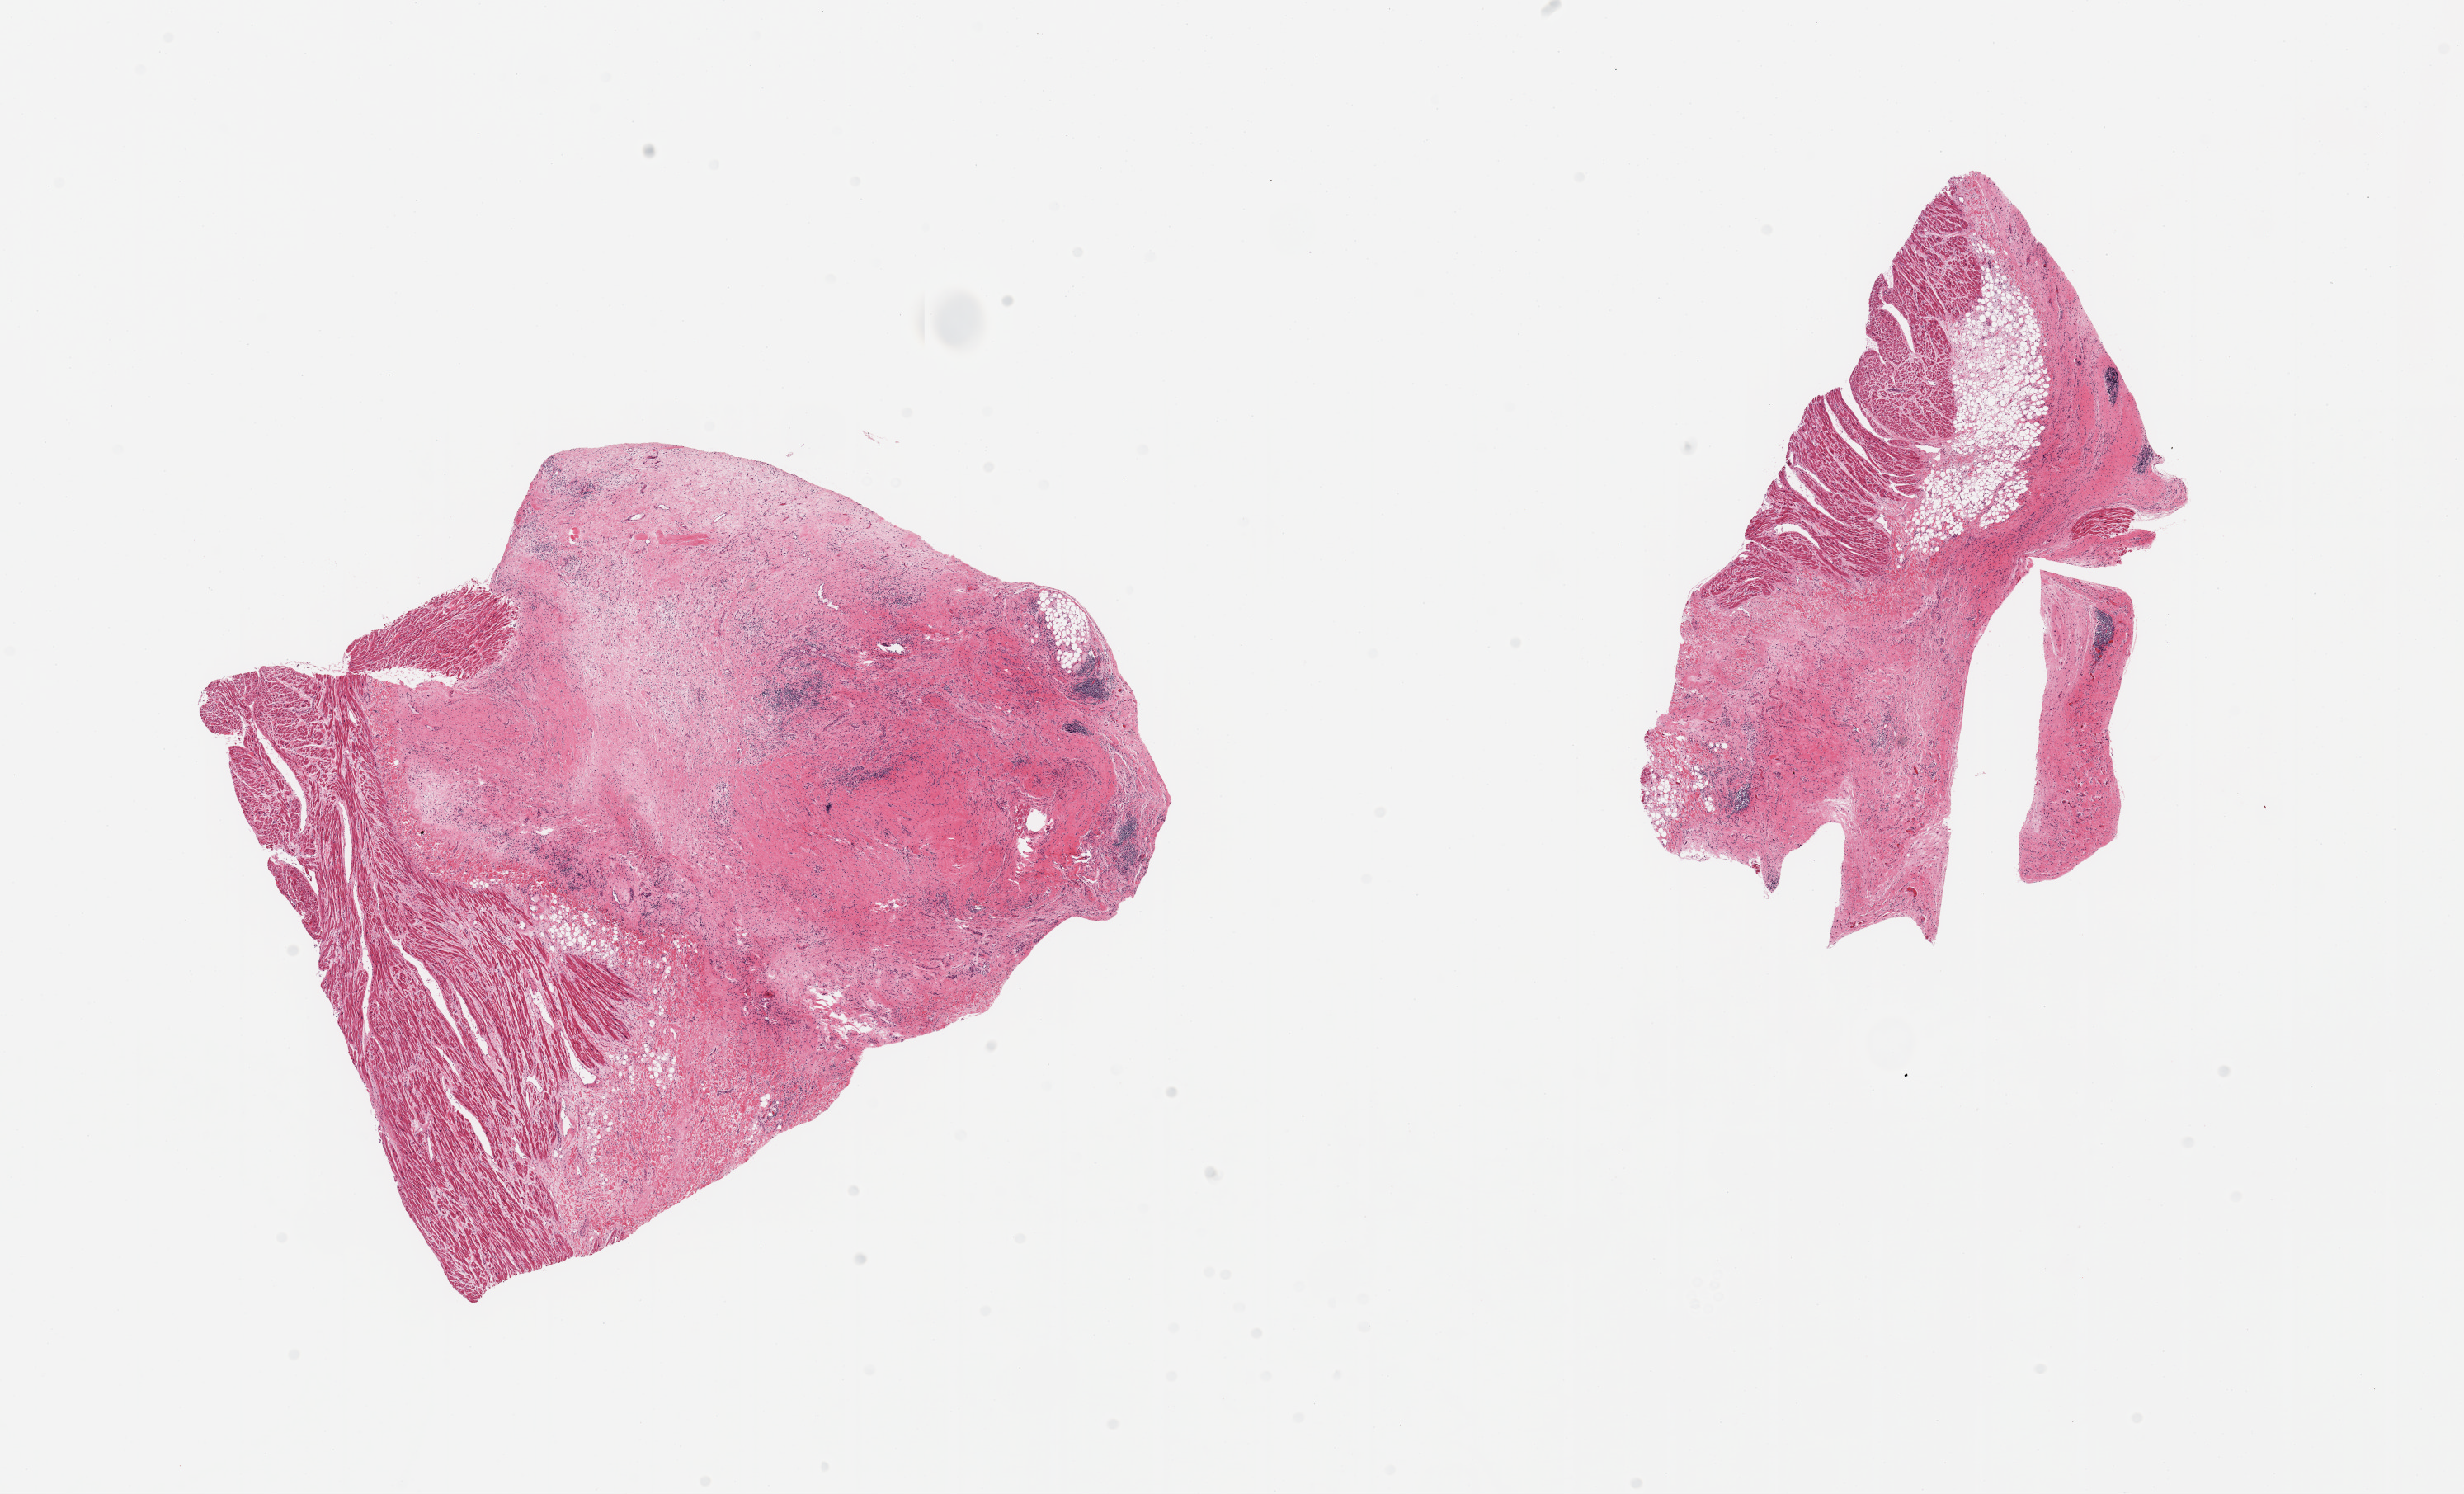
Whole-slide image, haematoxylin and eosin stain, whole scanned area (about 23.6 x 14.3 mm, from a 20x scan) shown as a low-resolution overview. PAXgene-fixed paraffin-embedded (PFPE) section. Target tissue: auricular appendage. Tissue donor sample. Female donor.
Reviewer comment on this tissue sample: 2 pieces; 30% muscle, remainder fibrofatty tissue.